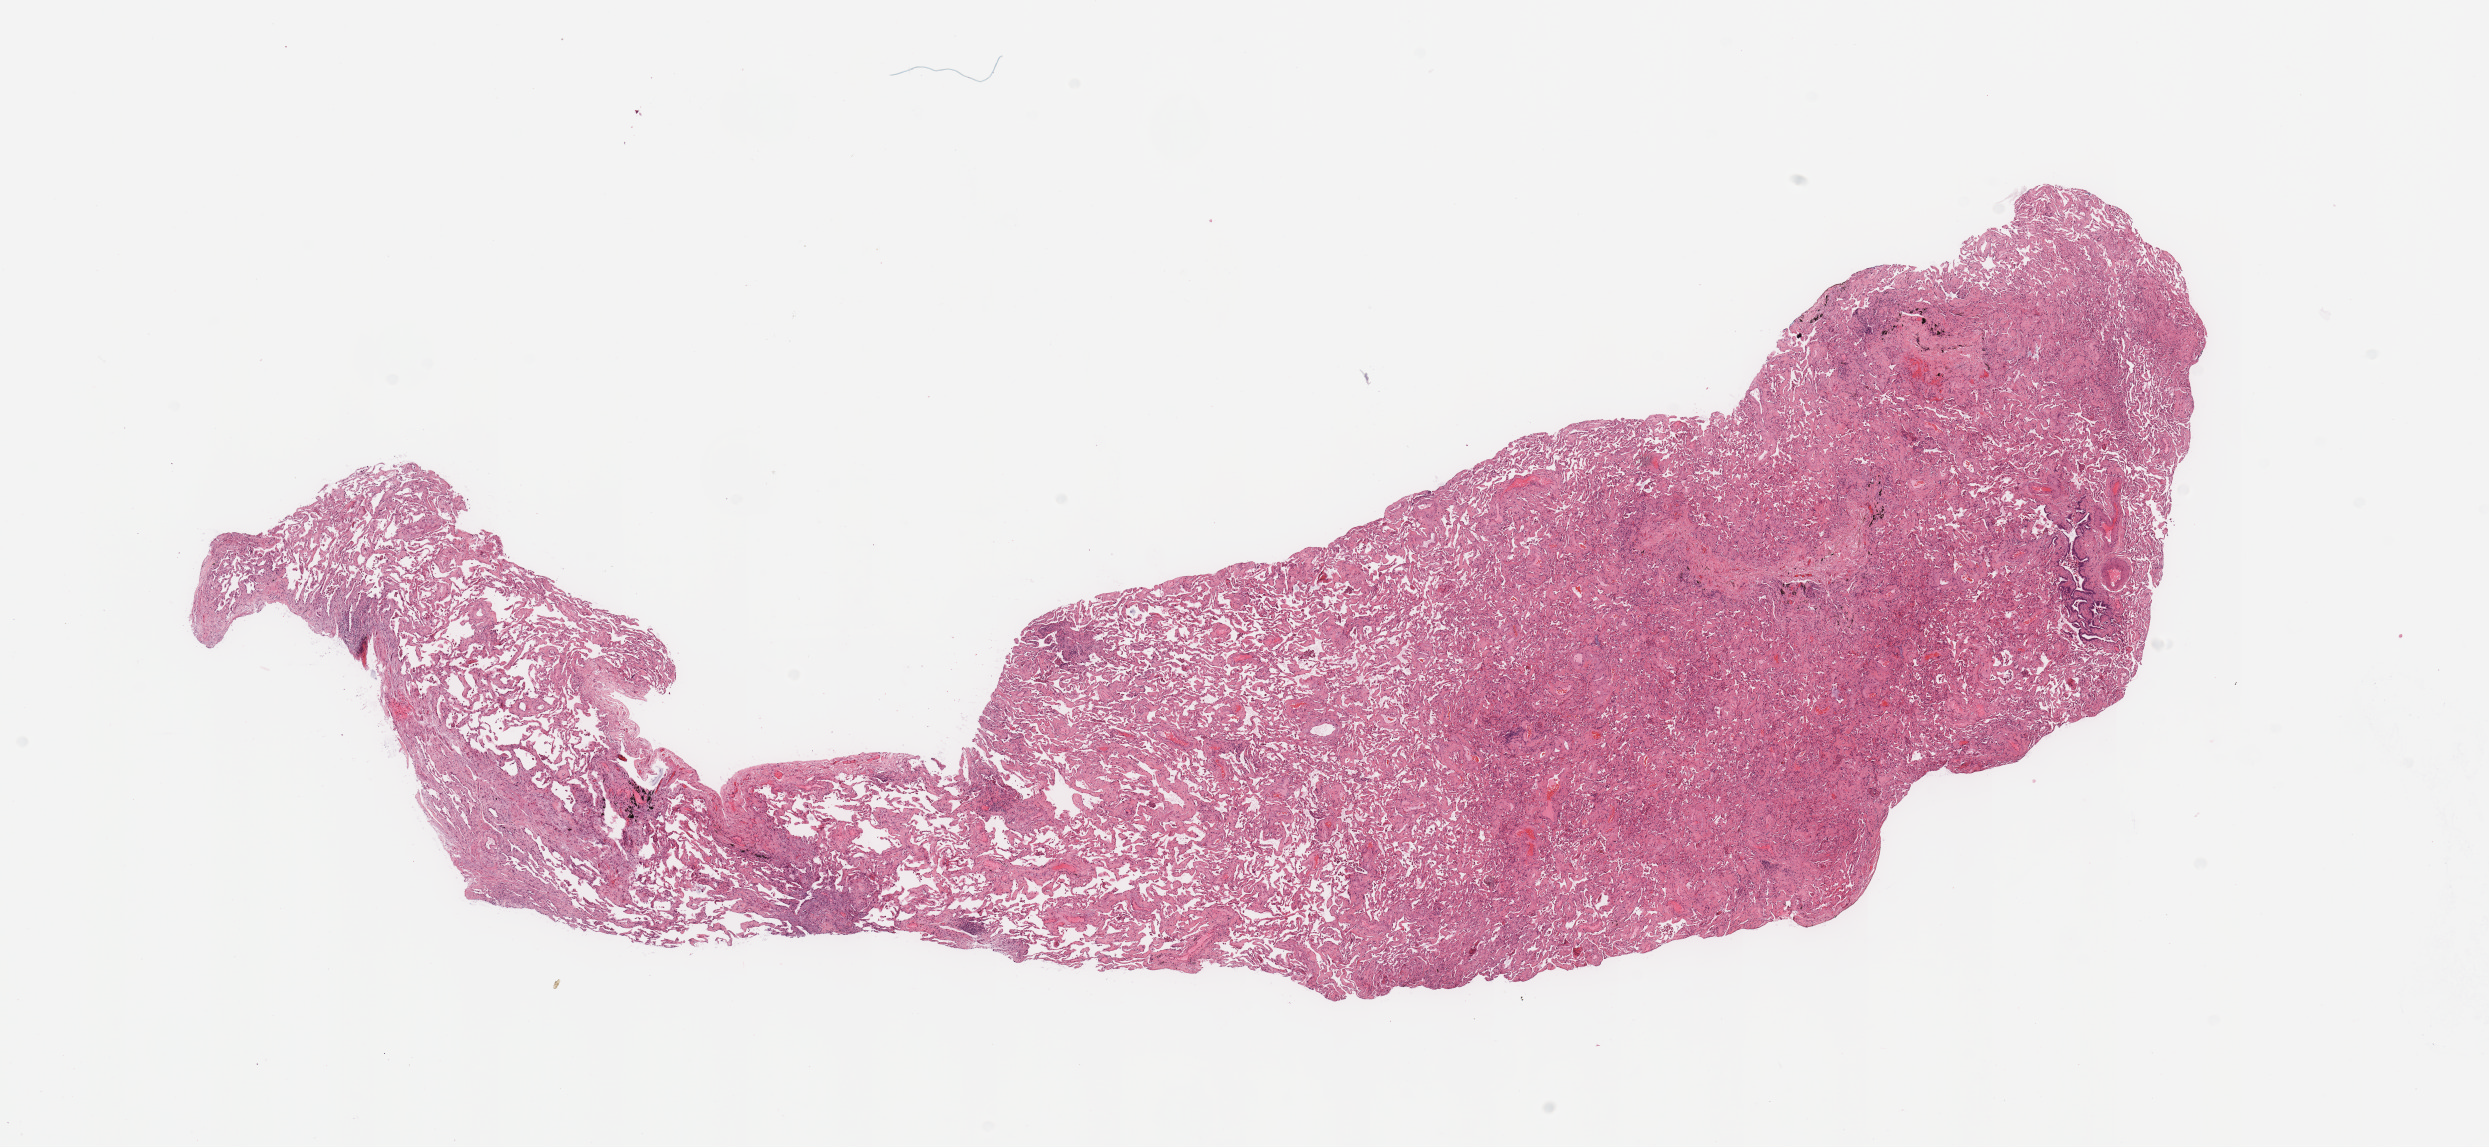
Whole-slide histology image, Hematoxylin and eosin (H&E) stained, shown as a low-resolution overview of the whole scanned area (about 19.7 x 9.1 mm, acquisition: 20x scan). Normal (non-tumour) tissue sample, sampled site: lung. Patient: female, age 78 years.
- this section: normal (non-tumour) tissue from the same patient
- patient diagnosis: Adenocarcinoma, NOS